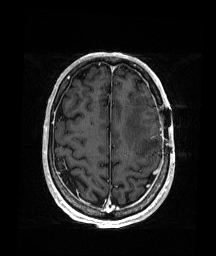
Brain MRI from a brain-tumour surgery series, one axial slice; slice 55 of 176 in the series (ordered by position); T1-weighted post-contrast; 216 × 256 image matrix. Case-level facts recorded for this patient, not image findings: histopathology: Glioblastoma; WHO grade: 4; IDH mutation: no.
Structures marked on this image (outlined manually by an expert reader):
- tumour: bounding box (x1, y1, x2, y2) in pixels: (151, 124, 157, 132)